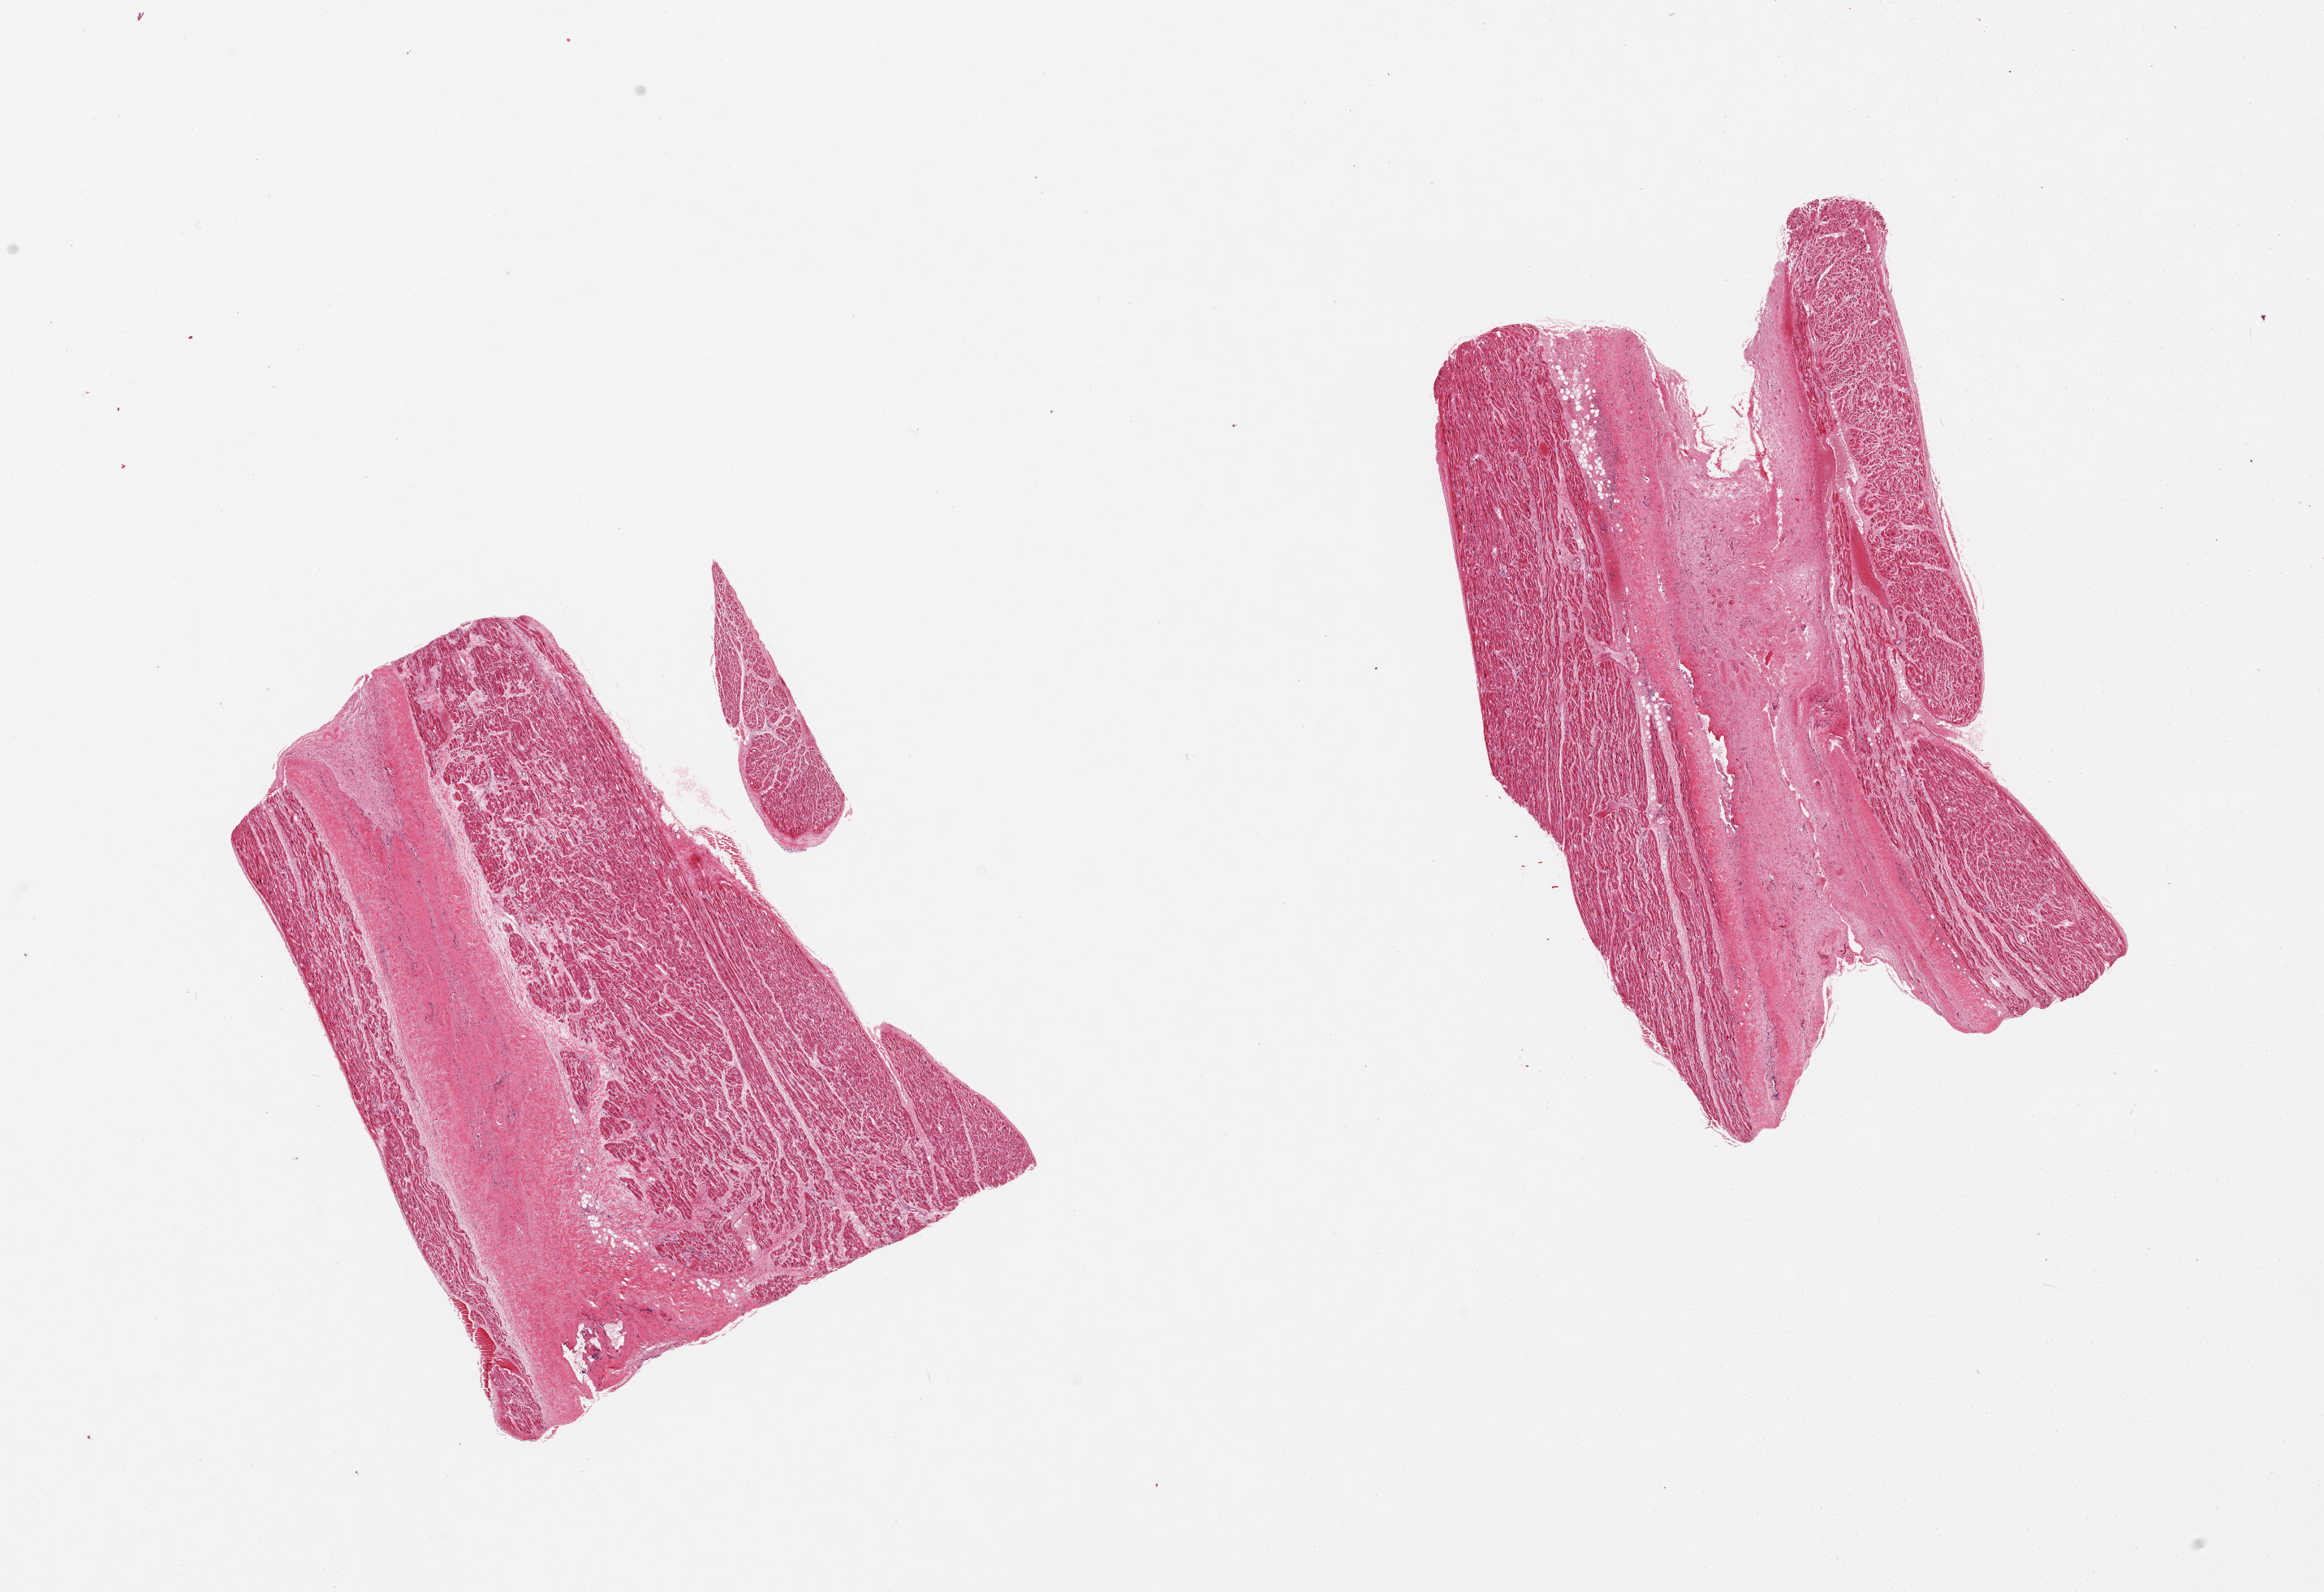
H&E whole-slide image — low-resolution overview of the scanned area, about 22.6 x 15.5 mm (from a 20x scan), PAXgene-fixed, paraffin-embedded tissue, sampled site (target tissue): auricular appendage, tissue donor sample. Donor sex: female.
Review note (as recorded): 2 pieces.